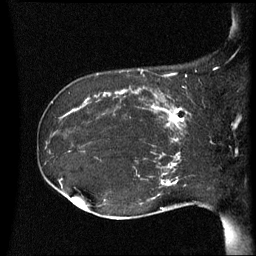
Breast MRI (dynamic contrast-enhanced), one sagittal slice. Slice 22 of 60 in the series (ordered by position). Dynamic contrast-enhanced series, image 2 of 3 at this slice position (ordered by acquisition). 1.5 T. TE 4.2 ms, TR 8.4 ms. 2.5 mm slice thickness. 256 × 256 image matrix, field of view 220 × 220 mm. Female patient, age 41 years. Case-level facts recorded for this patient, not image findings: setting: breast cancer imaged before/during neoadjuvant chemotherapy; receptor status: HER2-positive.
Structures marked on this image (semi-automatically segmented with operator editing):
- analysis volume of interest (the breast-tissue region the enhancement analysis was run in; not a lesion): box from (x=122, y=84) to (x=195, y=137) px
- tumour enhancement mask (voxels above the 70 % enhancement threshold inside the analysis volume of interest): (x=122, y=90)–(x=191, y=137)